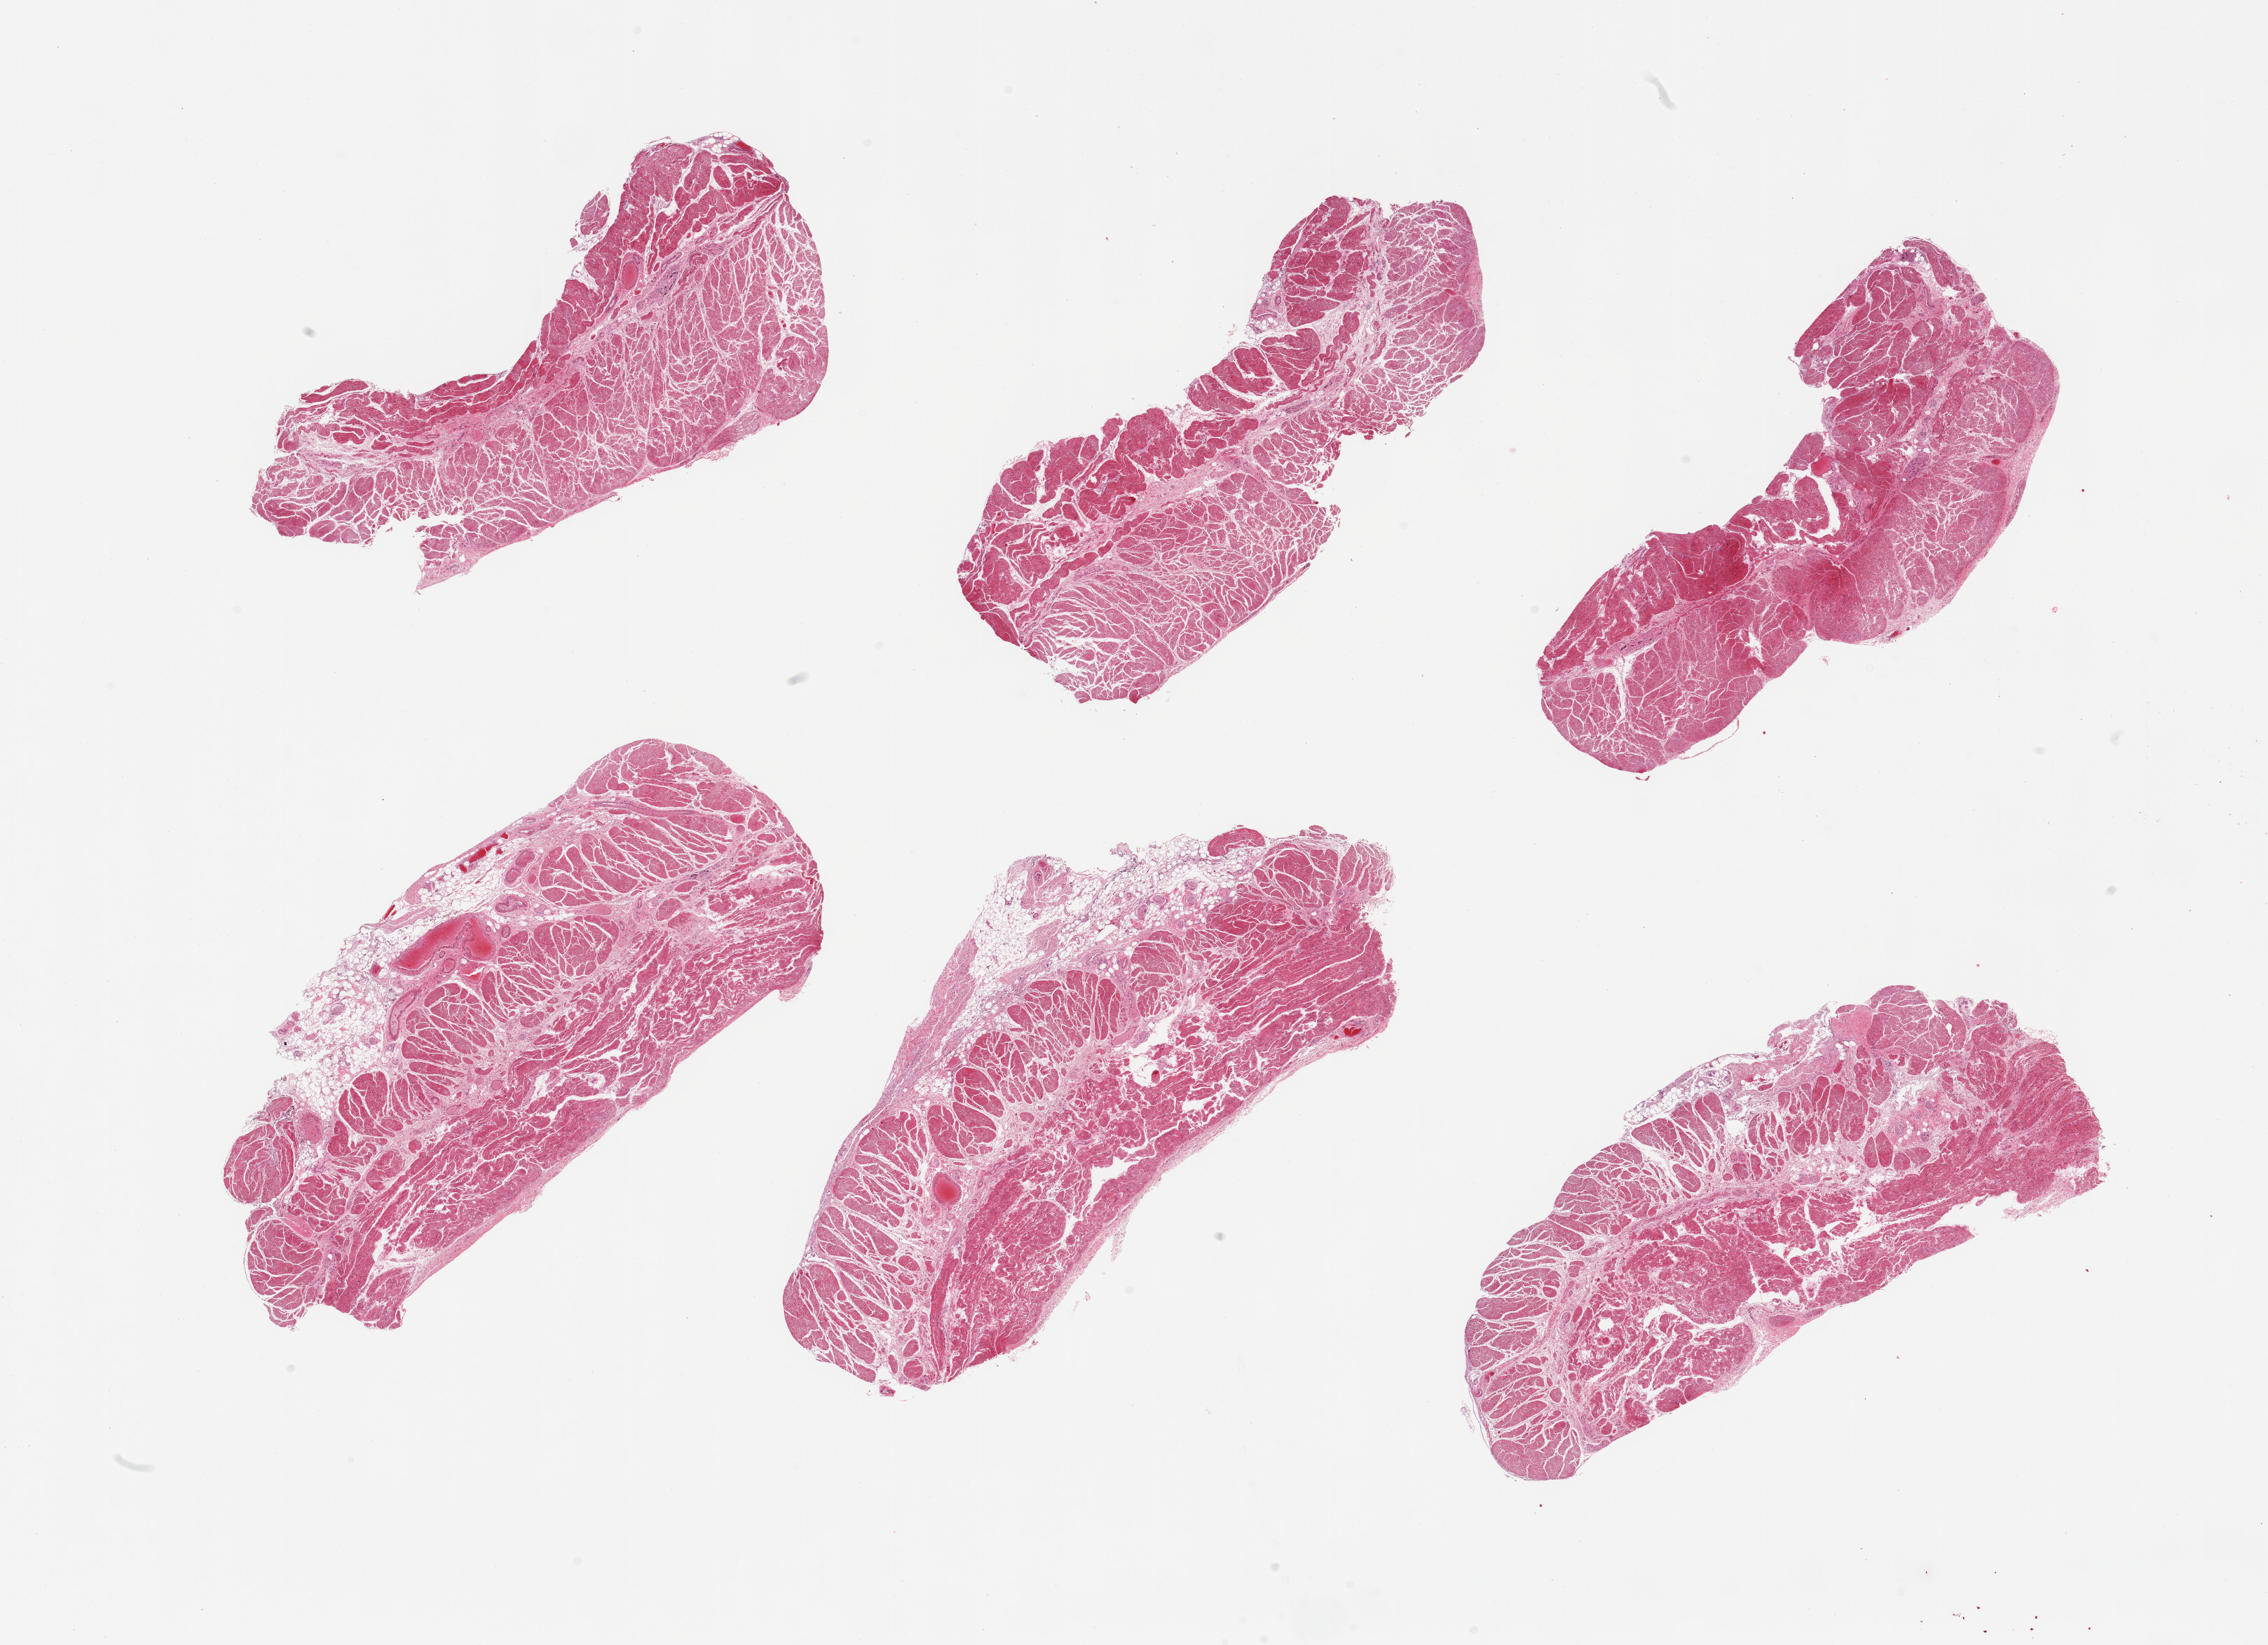
Digitized hematoxylin and eosin (H&E)-stained section, brightfield, a low-resolution overview of the entire scanned area, about 25.6 x 18.6 mm (from a 20x scan). PAXgene-fixed paraffin-embedded (PFPE) section. Sampled site (target tissue): esophageal muscle. Donor tissue sample. Donor sex: male.
Pathologist's review note for this sample: 6 pieces; targeted muscularis present; two pieces contain ~5 to 10% external fat.